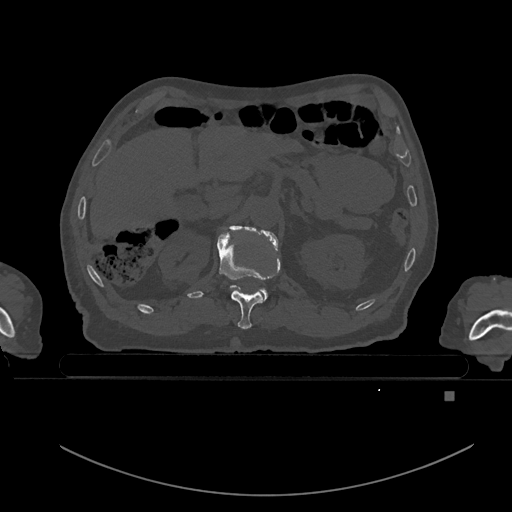
CT including the spine, one axial slice; position 3 of 969 along the scan axis; bone window (W 1800 / L 400 HU); 0.5 mm slice thickness; 512 × 512 image matrix, field of view 456 × 456 mm. Male patient, age 82 years. From the clinical record (not read from this slice): primary cancer: prostate.
Annotated regions visible in this slice (semi-automatically segmented with operator editing):
- T11 vertebra: bounding box [x1, y1, x2, y2] px = [217, 227, 277, 329]